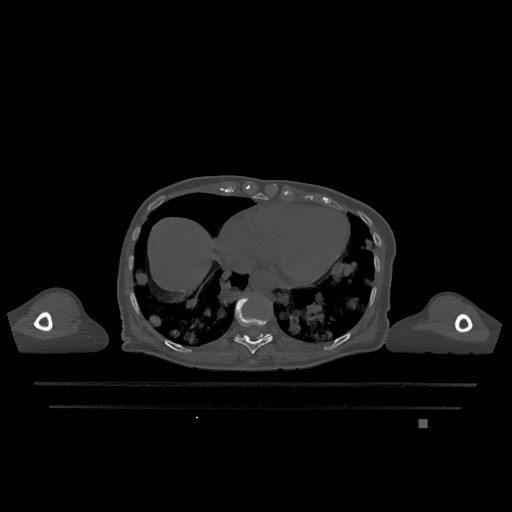
CT including the spine, one axial slice; position 630 of 1317 along the scan axis; bone window (W 1800 / L 400 HU); 512 × 512 image matrix, field of view 500 × 500 mm. Female patient, age 74 years. From the clinical record (not read from this slice): primary cancer: lung.
Structures marked on this image (semi-automatically segmented with operator editing):
- T10 vertebra: bounding box [x1, y1, x2, y2] px = [234, 297, 273, 354]
- T11 vertebra: [266, 334, 270, 337]